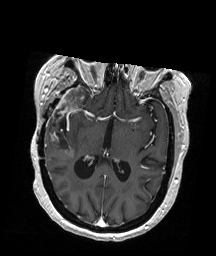
Brain MRI from a brain-tumour surgery series, one axial slice; slice 104 of 192 in the series (ordered by position); T1-weighted post-contrast; 1 mm slice thickness; 216 × 256 image matrix, field of view 211 × 250 mm. From the clinical record (not read from this slice): histopathology: Glioblastoma; WHO grade: 4; IDH mutation: no; tumour location: Right Temporal.
Outlined on this slice (outlined manually by an expert reader):
- tumour: box from (x=49, y=87) to (x=87, y=140) px